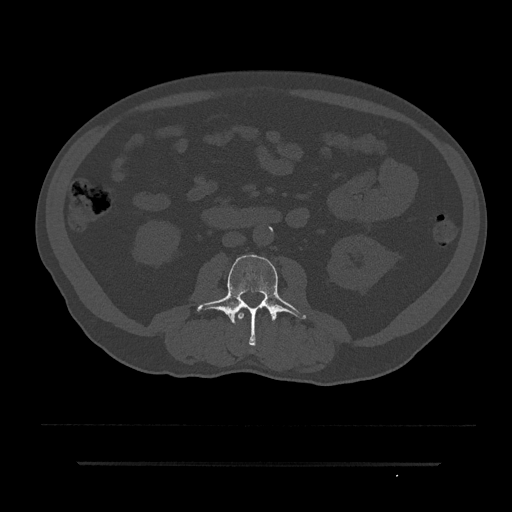
CT including the spine, one axial slice. Slice 13 of 797 in the series (ordered by position). Reconstruction kernel Br40s/3. 120 kVp. Bone window (W 1800 / L 400 HU). 0.5 mm slice thickness. 512 × 512 image matrix, field of view 464 × 464 mm. Patient: male, 59 years. Case-level facts recorded for this patient, not image findings: primary cancer: bile ducts.
Structures marked on this image (semi-automatically segmented with operator editing):
- L2 vertebra: bounding box <238,309,244,320> (left, top, right, bottom; pixels)
- L3 vertebra: <197,254,306,346>